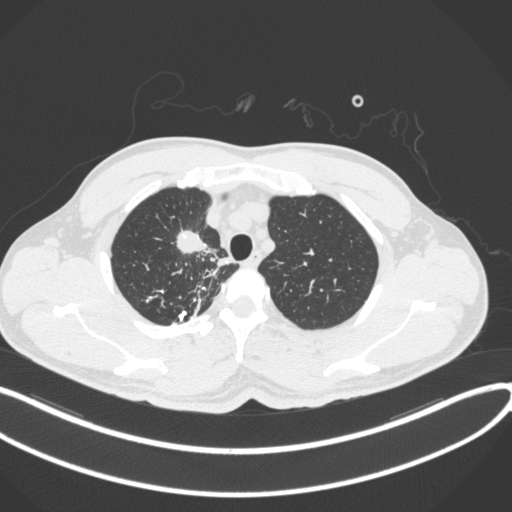
Chest CT, one axial slice; position 311 of 391 along the scan axis; reconstruction kernel B31f; 120 kVp; lung window (W 1500 / L -600 HU); 1 mm slice thickness; 512 × 512 image matrix, field of view 400 × 400 mm. Patient: male, 48 years. Case-level facts recorded for this patient, not image findings: clinical TNM (as recorded): T1c N1 M1.
Annotated regions visible in this slice (rectangle marked by the reading radiologist):
- lung tumour (recorded histology: adenocarcinoma): bounding box <172,221,209,259> (left, top, right, bottom; pixels)